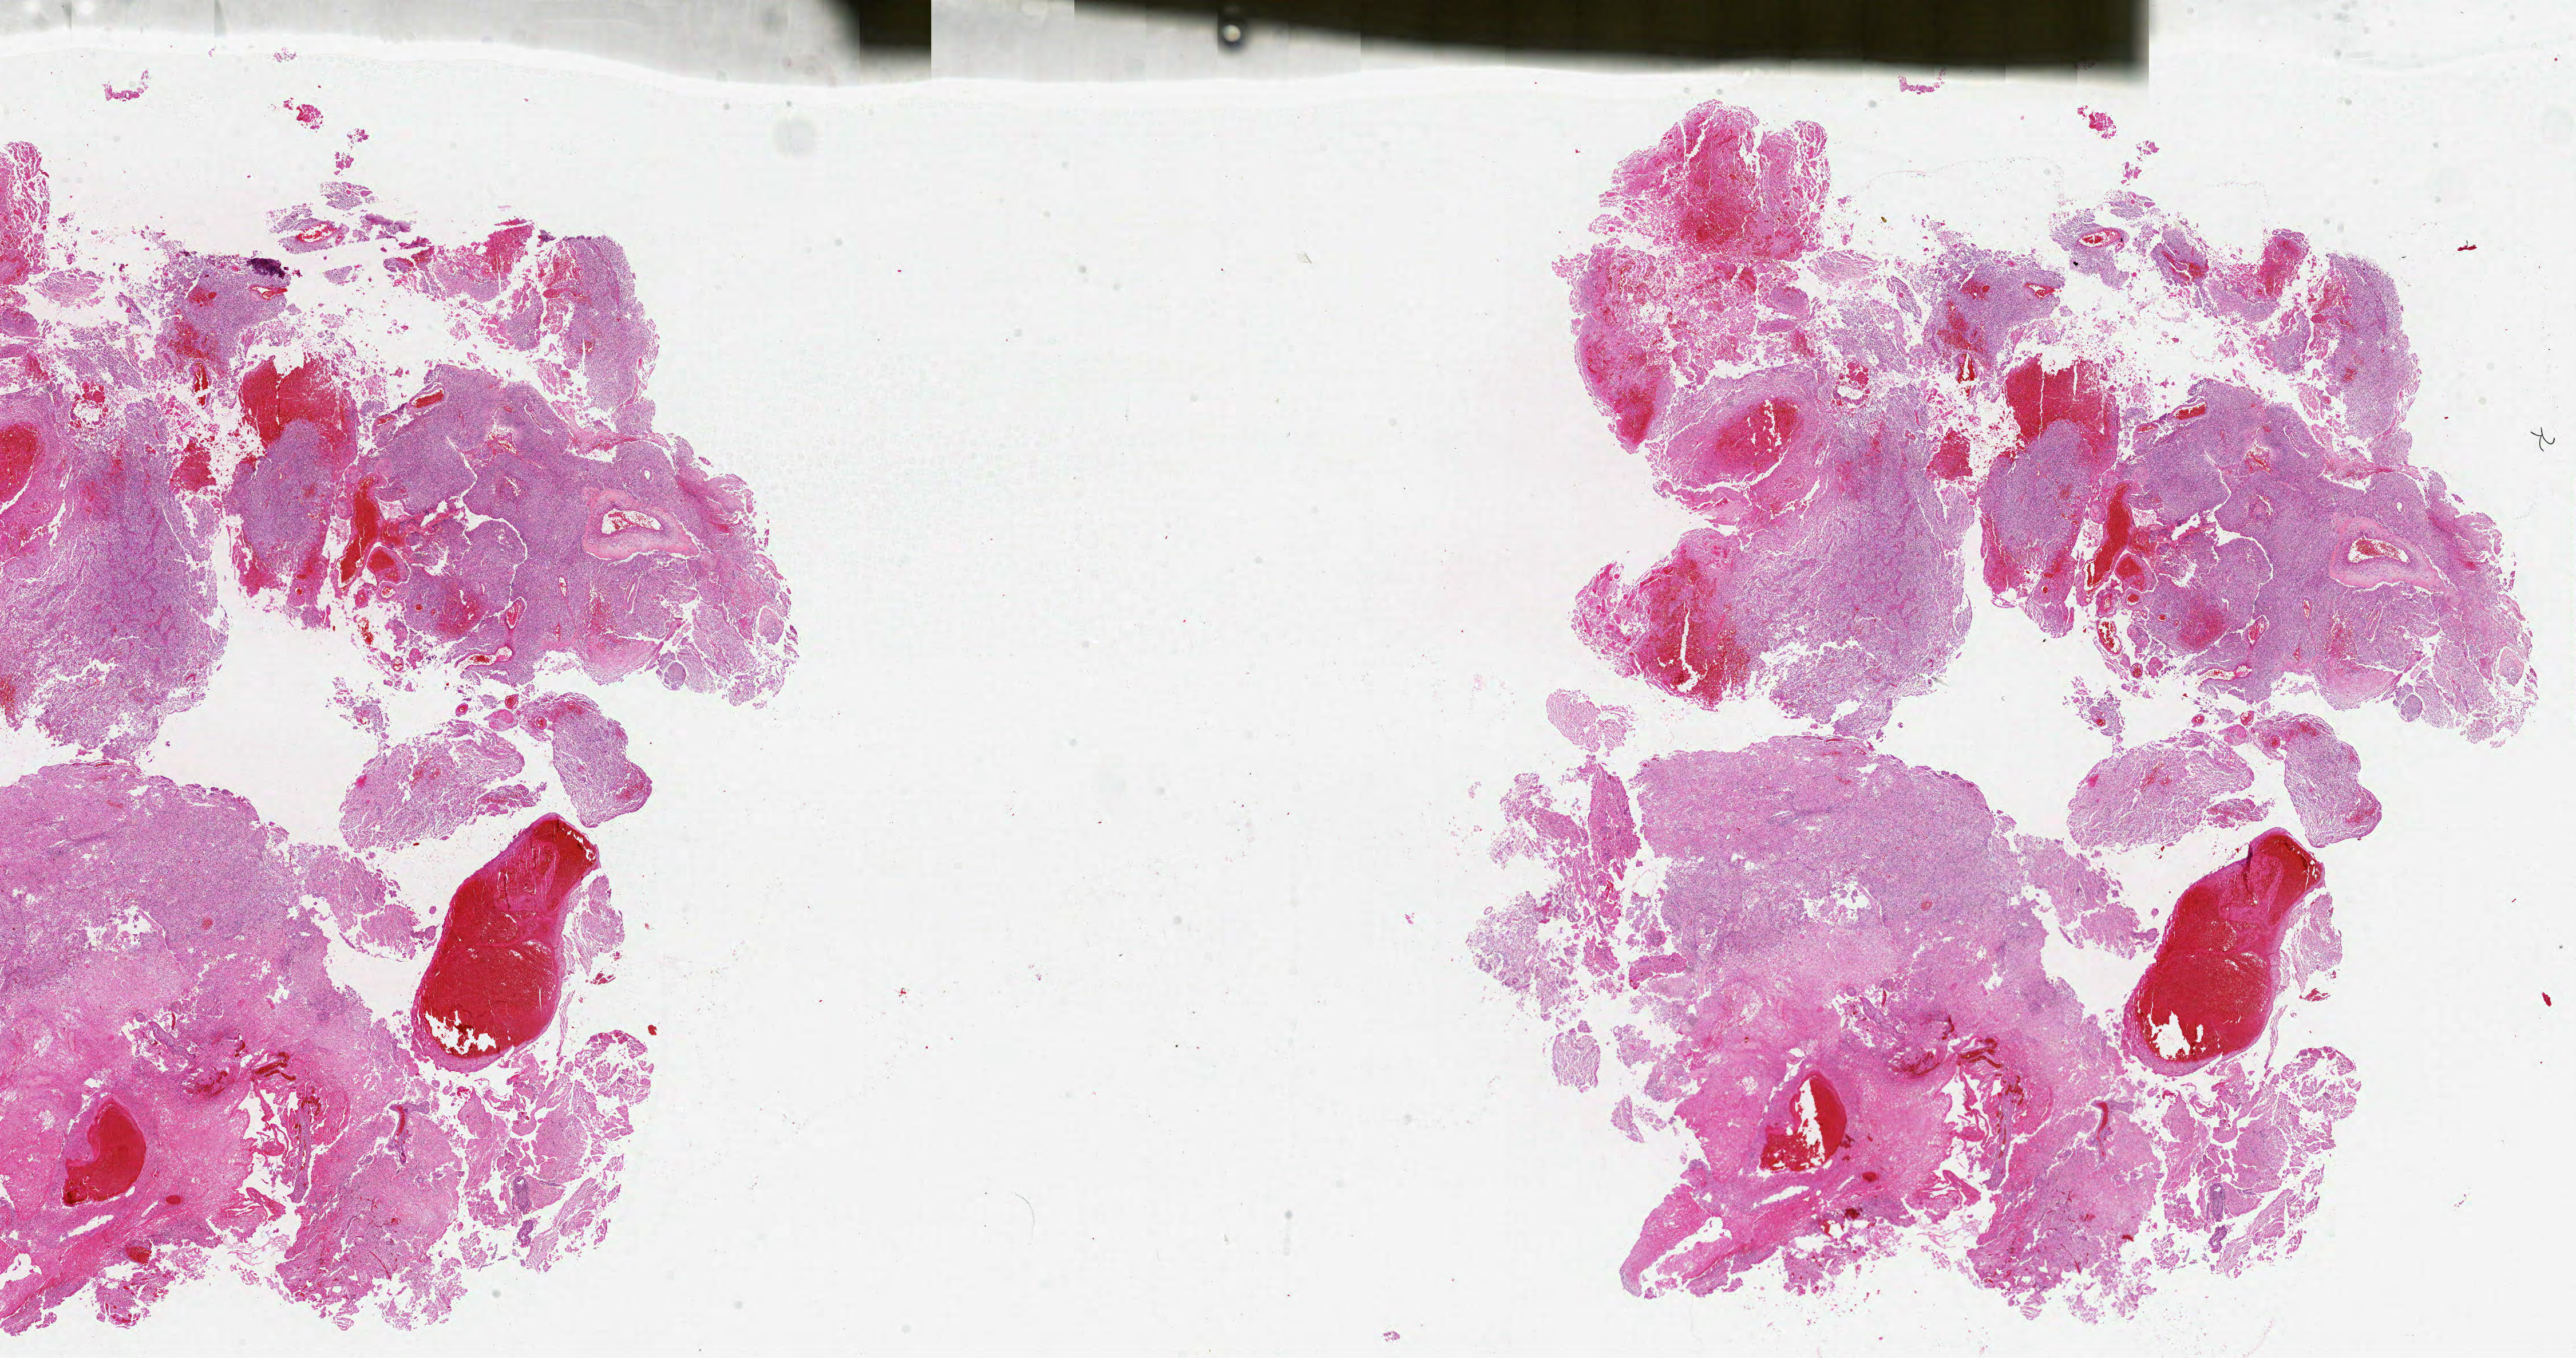
Hematoxylin and eosin (H&E) stained whole-slide image — whole scanned area (about 36.0 x 19.0 mm) shown as a low-resolution overview; FFPE section; sample: primary tumour, brain. Patient: male, age at initial diagnosis 53 years.
• histologic diagnosis: Glioblastoma